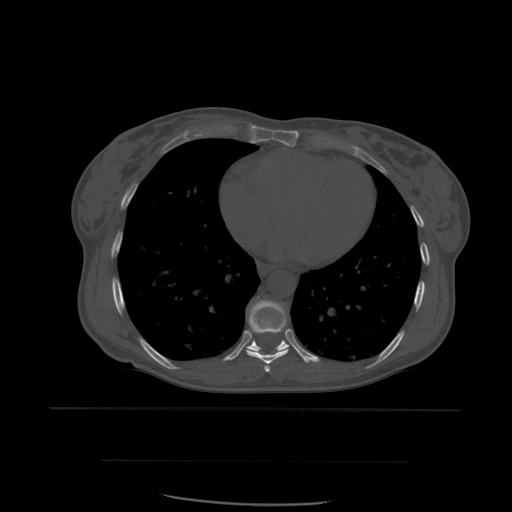
CT including the spine, one axial slice. Position 349 of 574 along the scan axis. Bone window (W 1800 / L 400 HU). 1.25 mm slice thickness. 512 × 512 image matrix, field of view 392 × 392 mm. Patient age 48 years. From the clinical record (not read from this slice): primary cancer: lung; vertebrae with lytic lesions (as recorded): T11.
Annotated regions visible in this slice (semi-automatic segmentation, software-assisted and operator-edited):
- T7 vertebra: bounding box <265,367,270,372> (left, top, right, bottom; pixels)
- T8 vertebra: <246,297,289,373>
- T9 vertebra: <232,302,313,363>